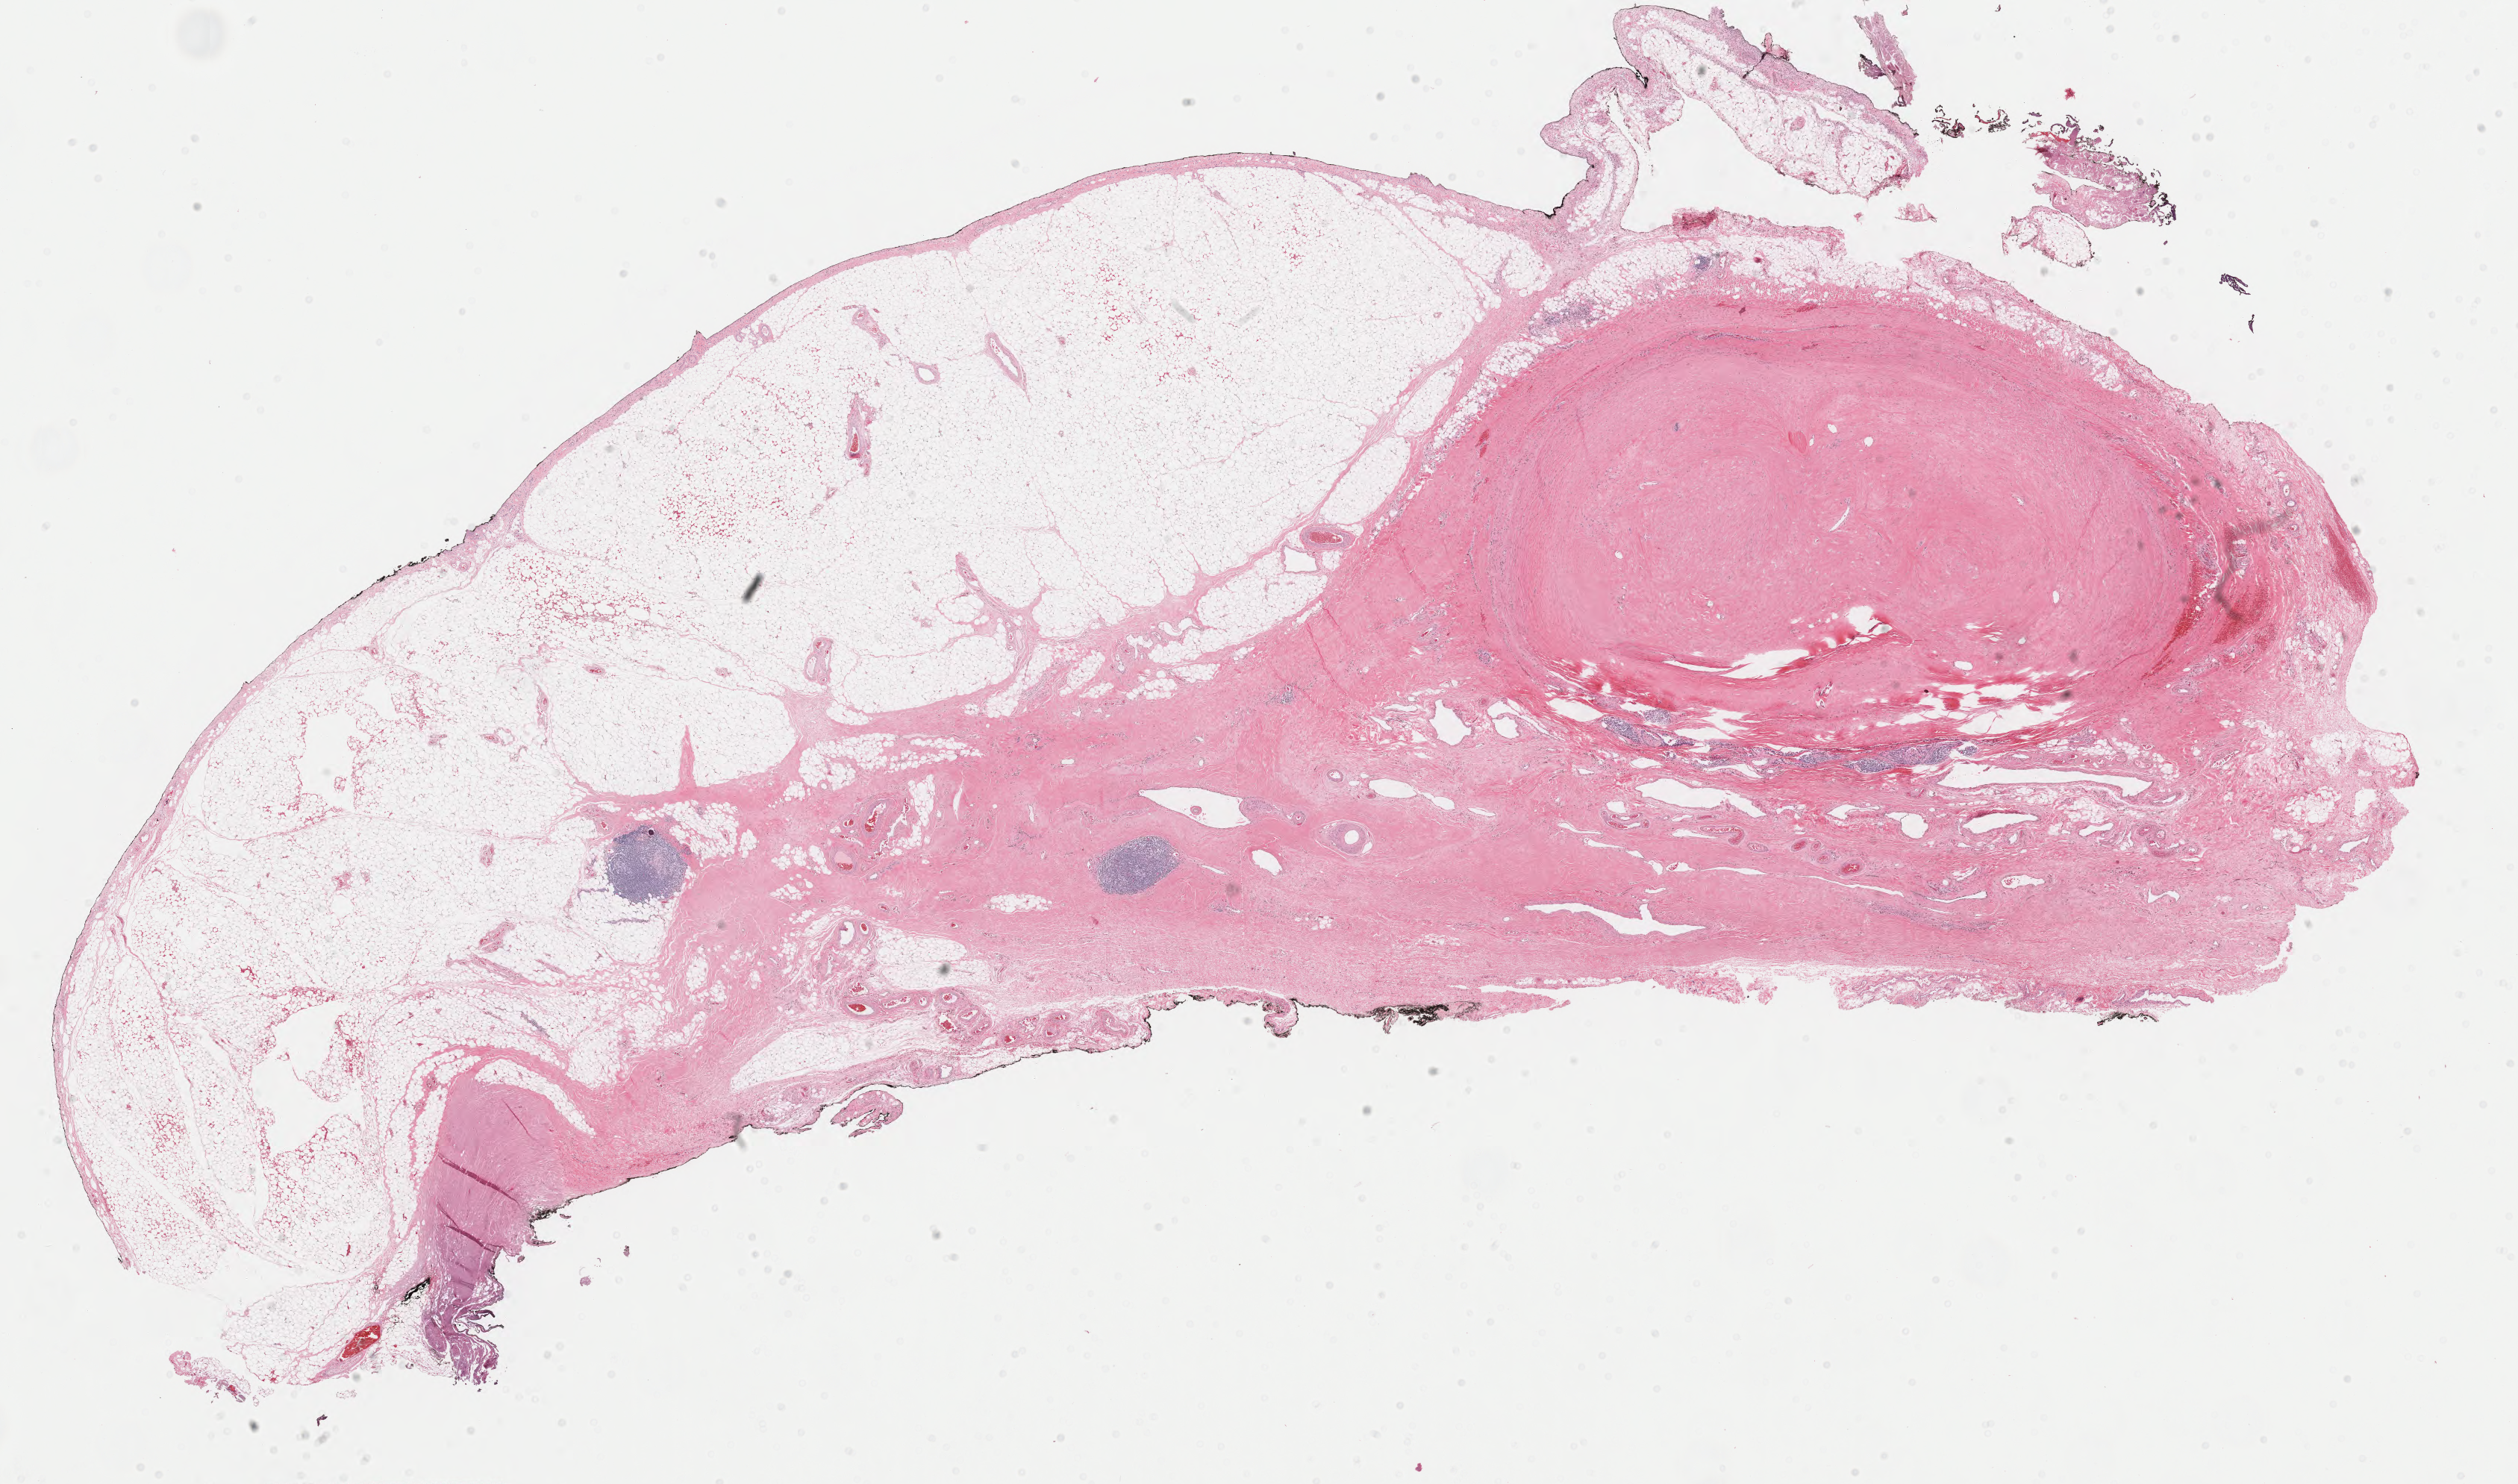
Digitized H&E-stained tissue section (whole slide), whole scanned area (about 26.8 x 15.8 mm, acquisition: 40x scan) shown as a low-resolution overview; formalin-fixed paraffin-embedded (FFPE) diagnostic section; thymus, primary tumour sample. Female patient; age at initial diagnosis 43 years.
Pathologic diagnosis: Thymoma, type B2, malignant.